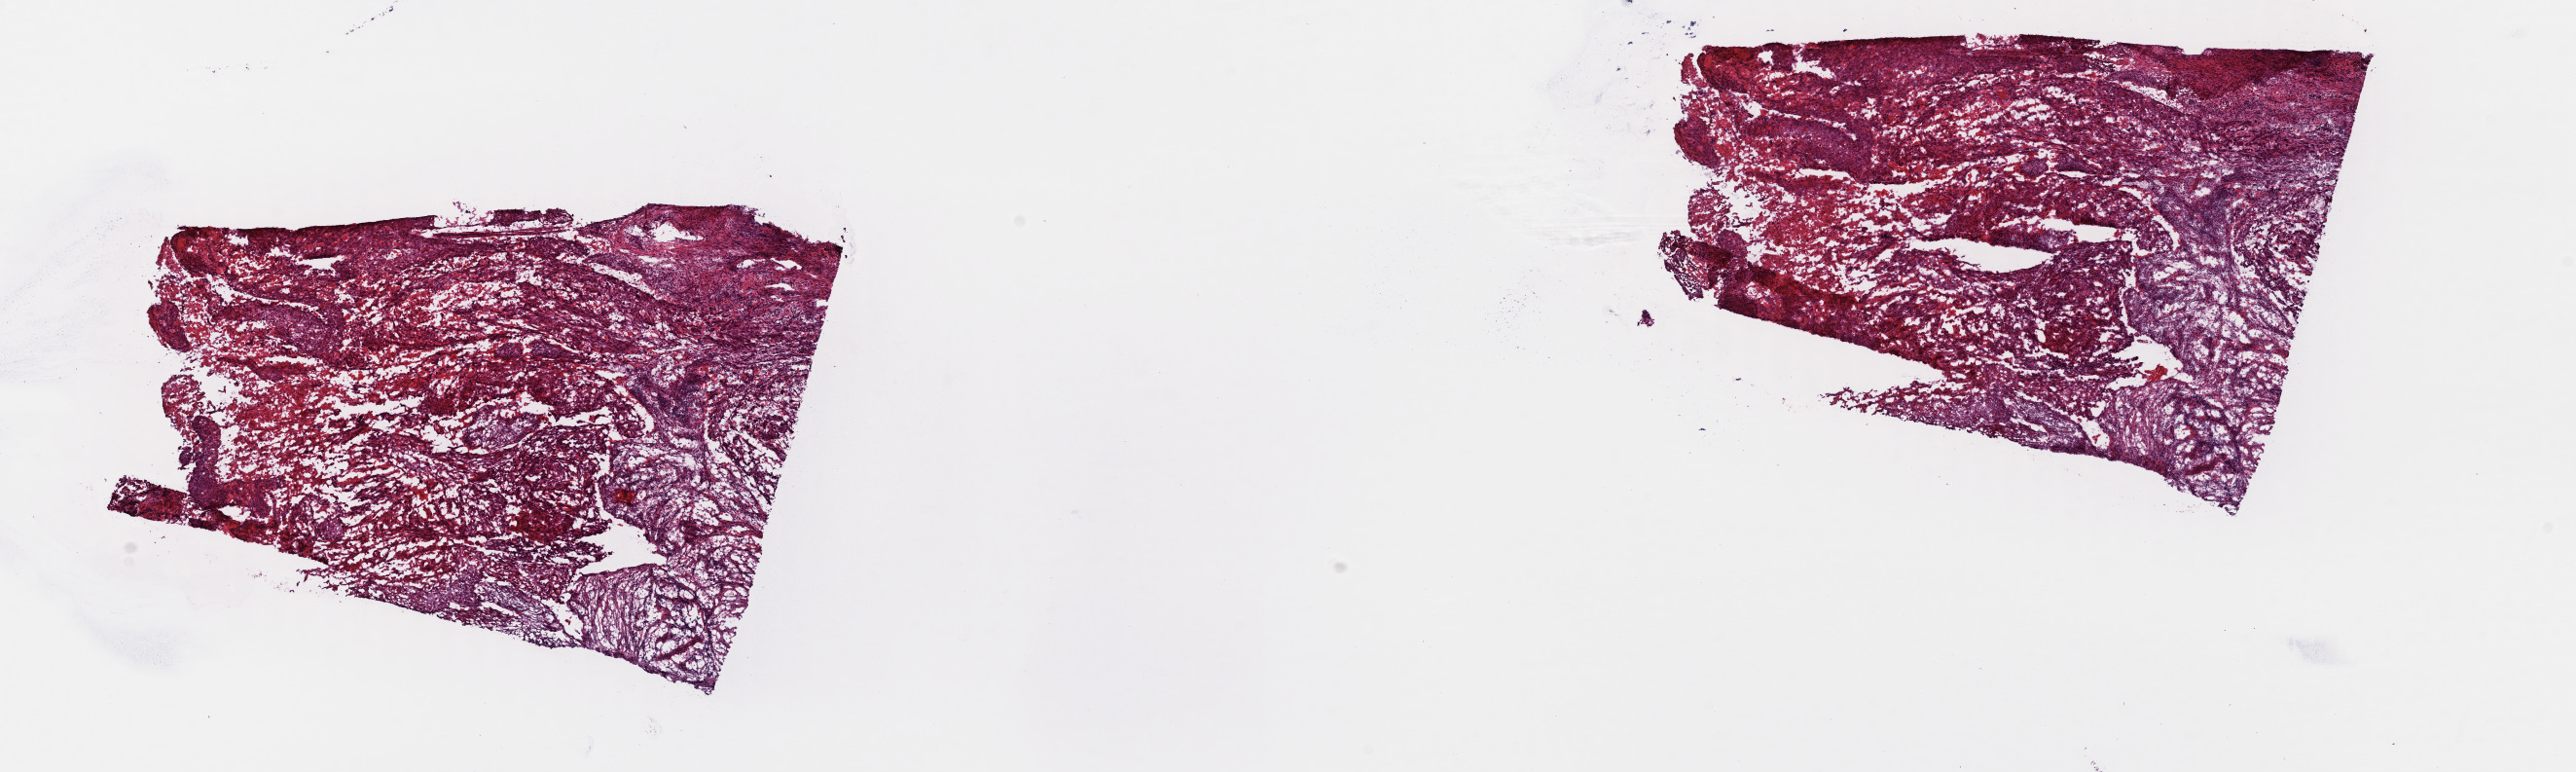
Whole-slide histology image, Hematoxylin and eosin (H&E) stained, whole scanned area (about 20.9 x 6.3 mm, from a 40x scan) shown as a low-resolution overview. Frozen section. Bladder, primary tumour sample. Patient: male, age at initial diagnosis 56 years. Histologic grade: high grade. Composition of this section per pathologist review: tumour cells 70%, tumour nuclei 80%, normal cells 0%, stromal cells 10%, necrosis 20%. Inflammatory infiltration, as recorded: lymphocyte infiltration 0%, monocyte infiltration 0%, neutrophil infiltration 0%.
AJCC pathologic stage: IV (6th edition). Lymph nodes positive (case pathology): 3 of 12 examined. Pathologic diagnosis: Transitional cell carcinoma (dome of bladder).